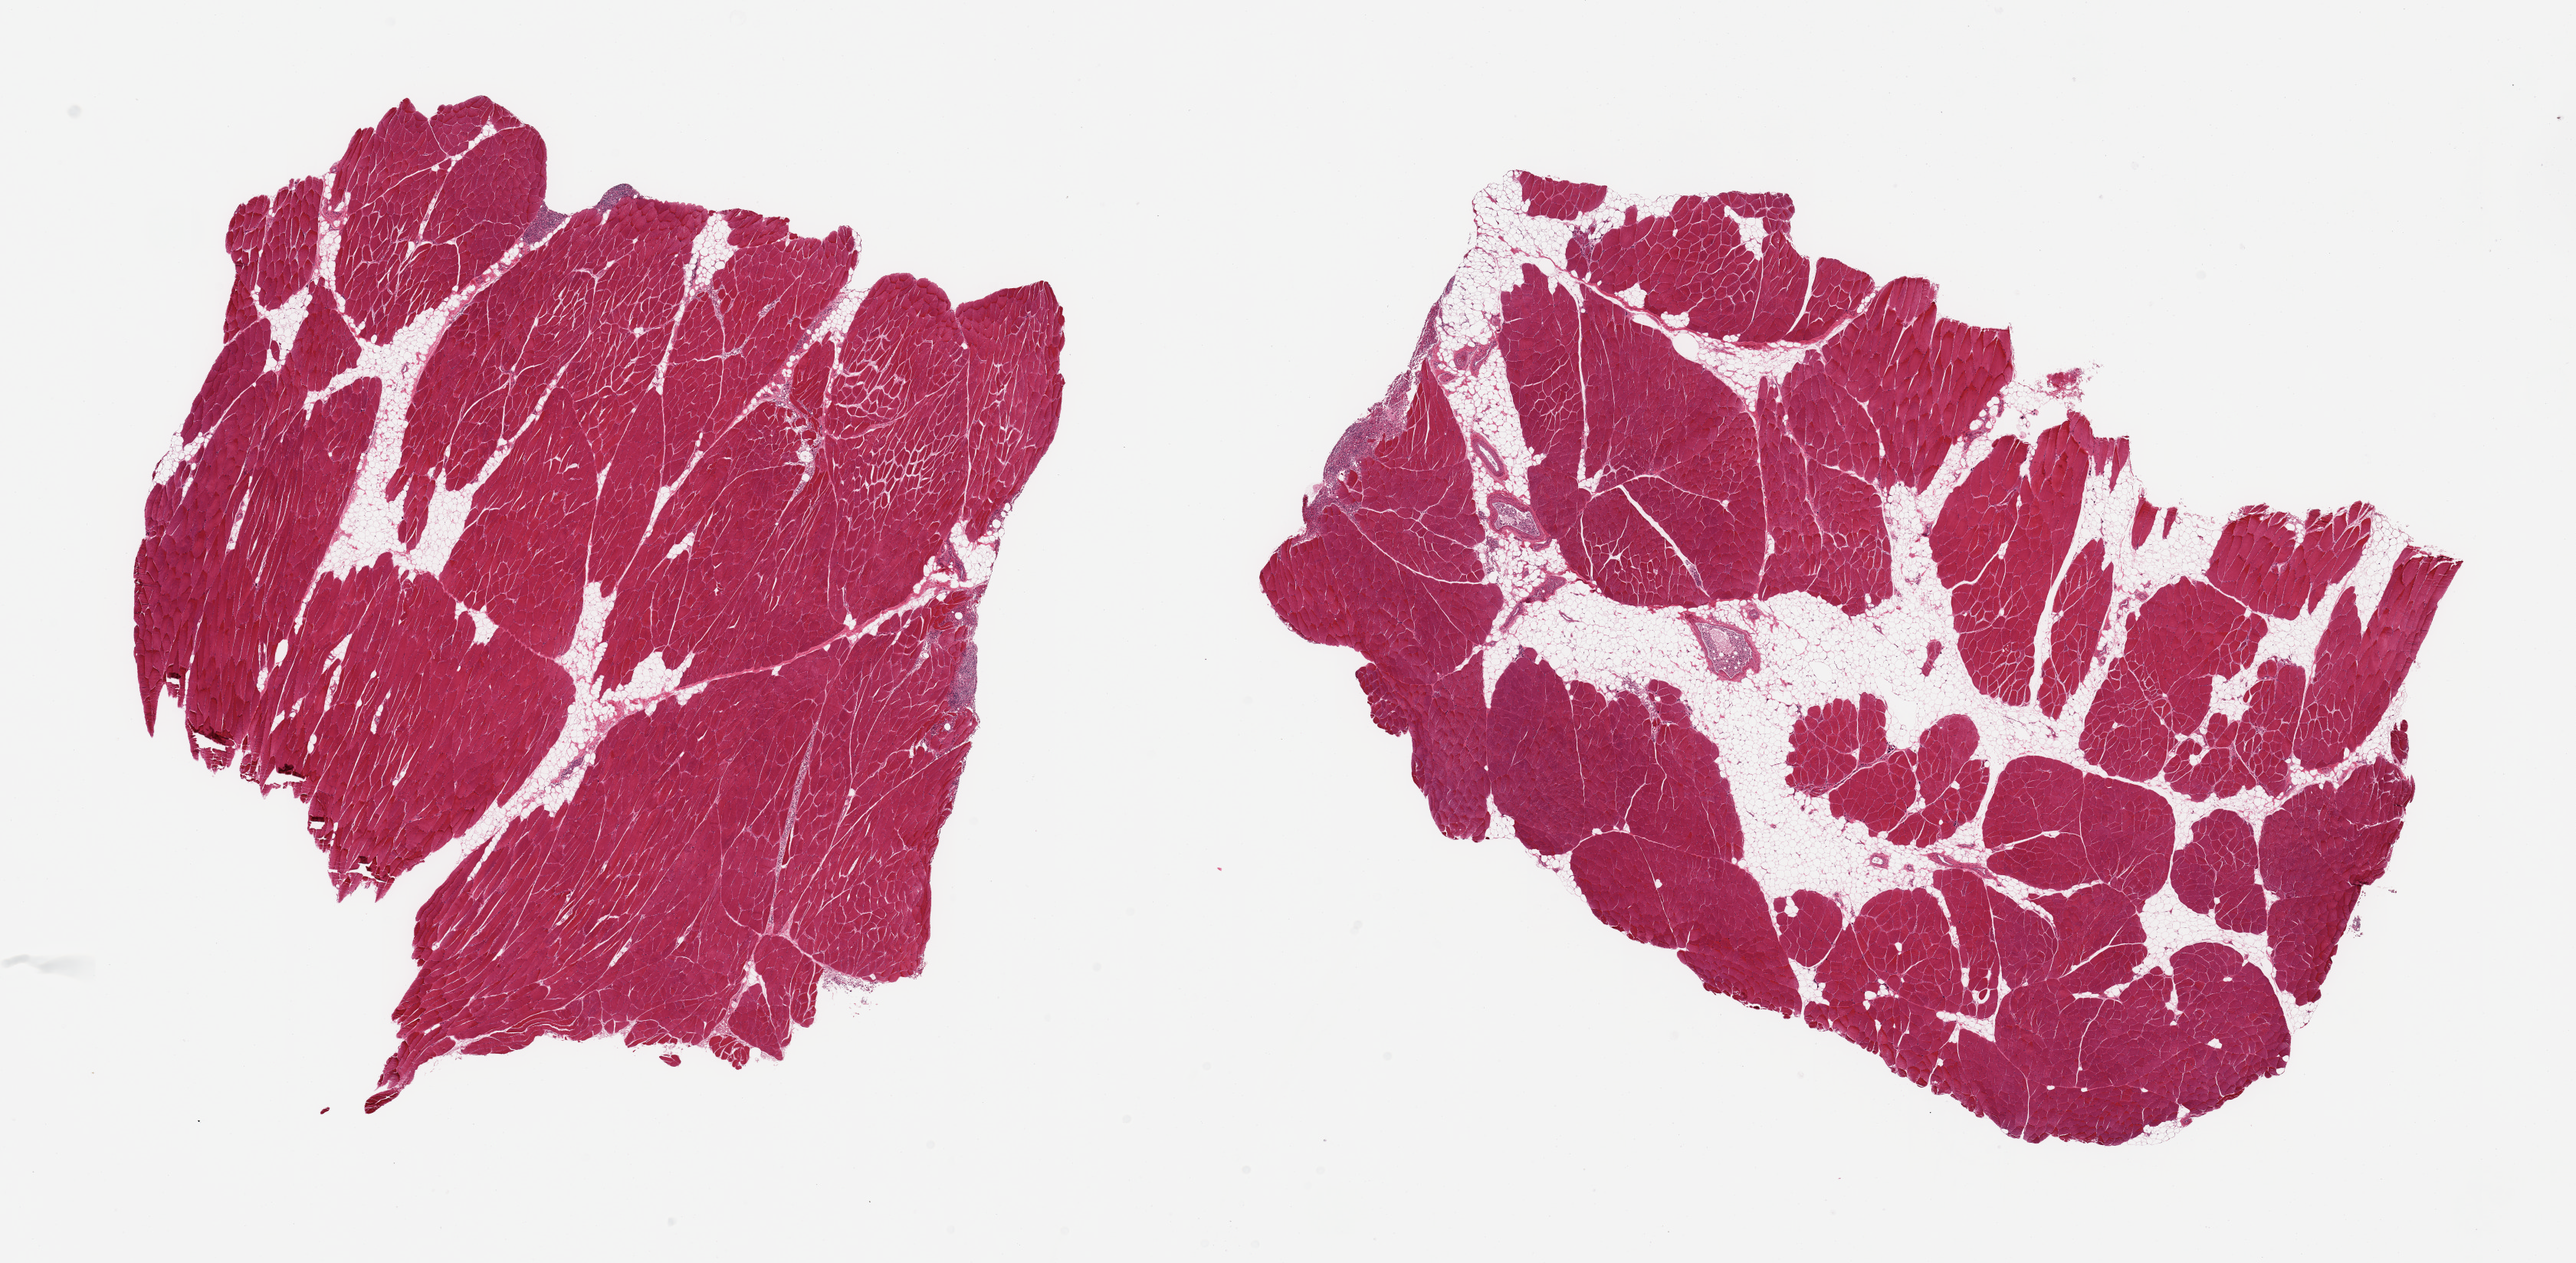
Whole-slide image, haematoxylin and eosin stain, brightfield, low-resolution overview of the scanned area, about 26.6 x 13.0 mm (slide scanned at 20x); PAXgene-fixed, paraffin-embedded tissue; sampled site (target tissue): skeletal muscle; donor tissue sample. Donor sex: female.
Pathologist's review note for this sample: 2 pieces; foci of splenic tissue carry-over on surface and ? in vessels; 40% & 10% internal fat.